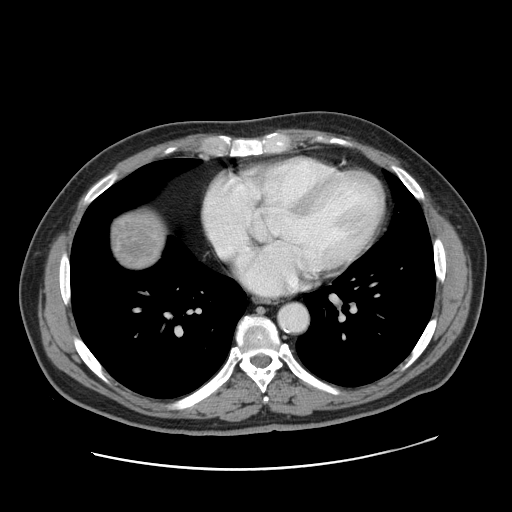
Contrast-enhanced abdominal CT, one axial slice; slice 166 of 178 in the series (ordered by position); intravenous contrast given; soft-tissue window (W 400 / L 40 HU); 512 × 512 image matrix, field of view 403 × 403 mm. Male patient, age 63 years. From the clinical record (not read from this slice): diagnosis: colorectal cancer liver metastases, imaged before liver resection; multiple liver metastases: yes; largest metastasis: 8 cm; disease in both lobes: yes.
Outlined on this slice (outlined manually by an expert reader):
- liver: bounding box <110,211,164,268> (left, top, right, bottom; pixels)
- liver metastasis: <113,214,164,269>